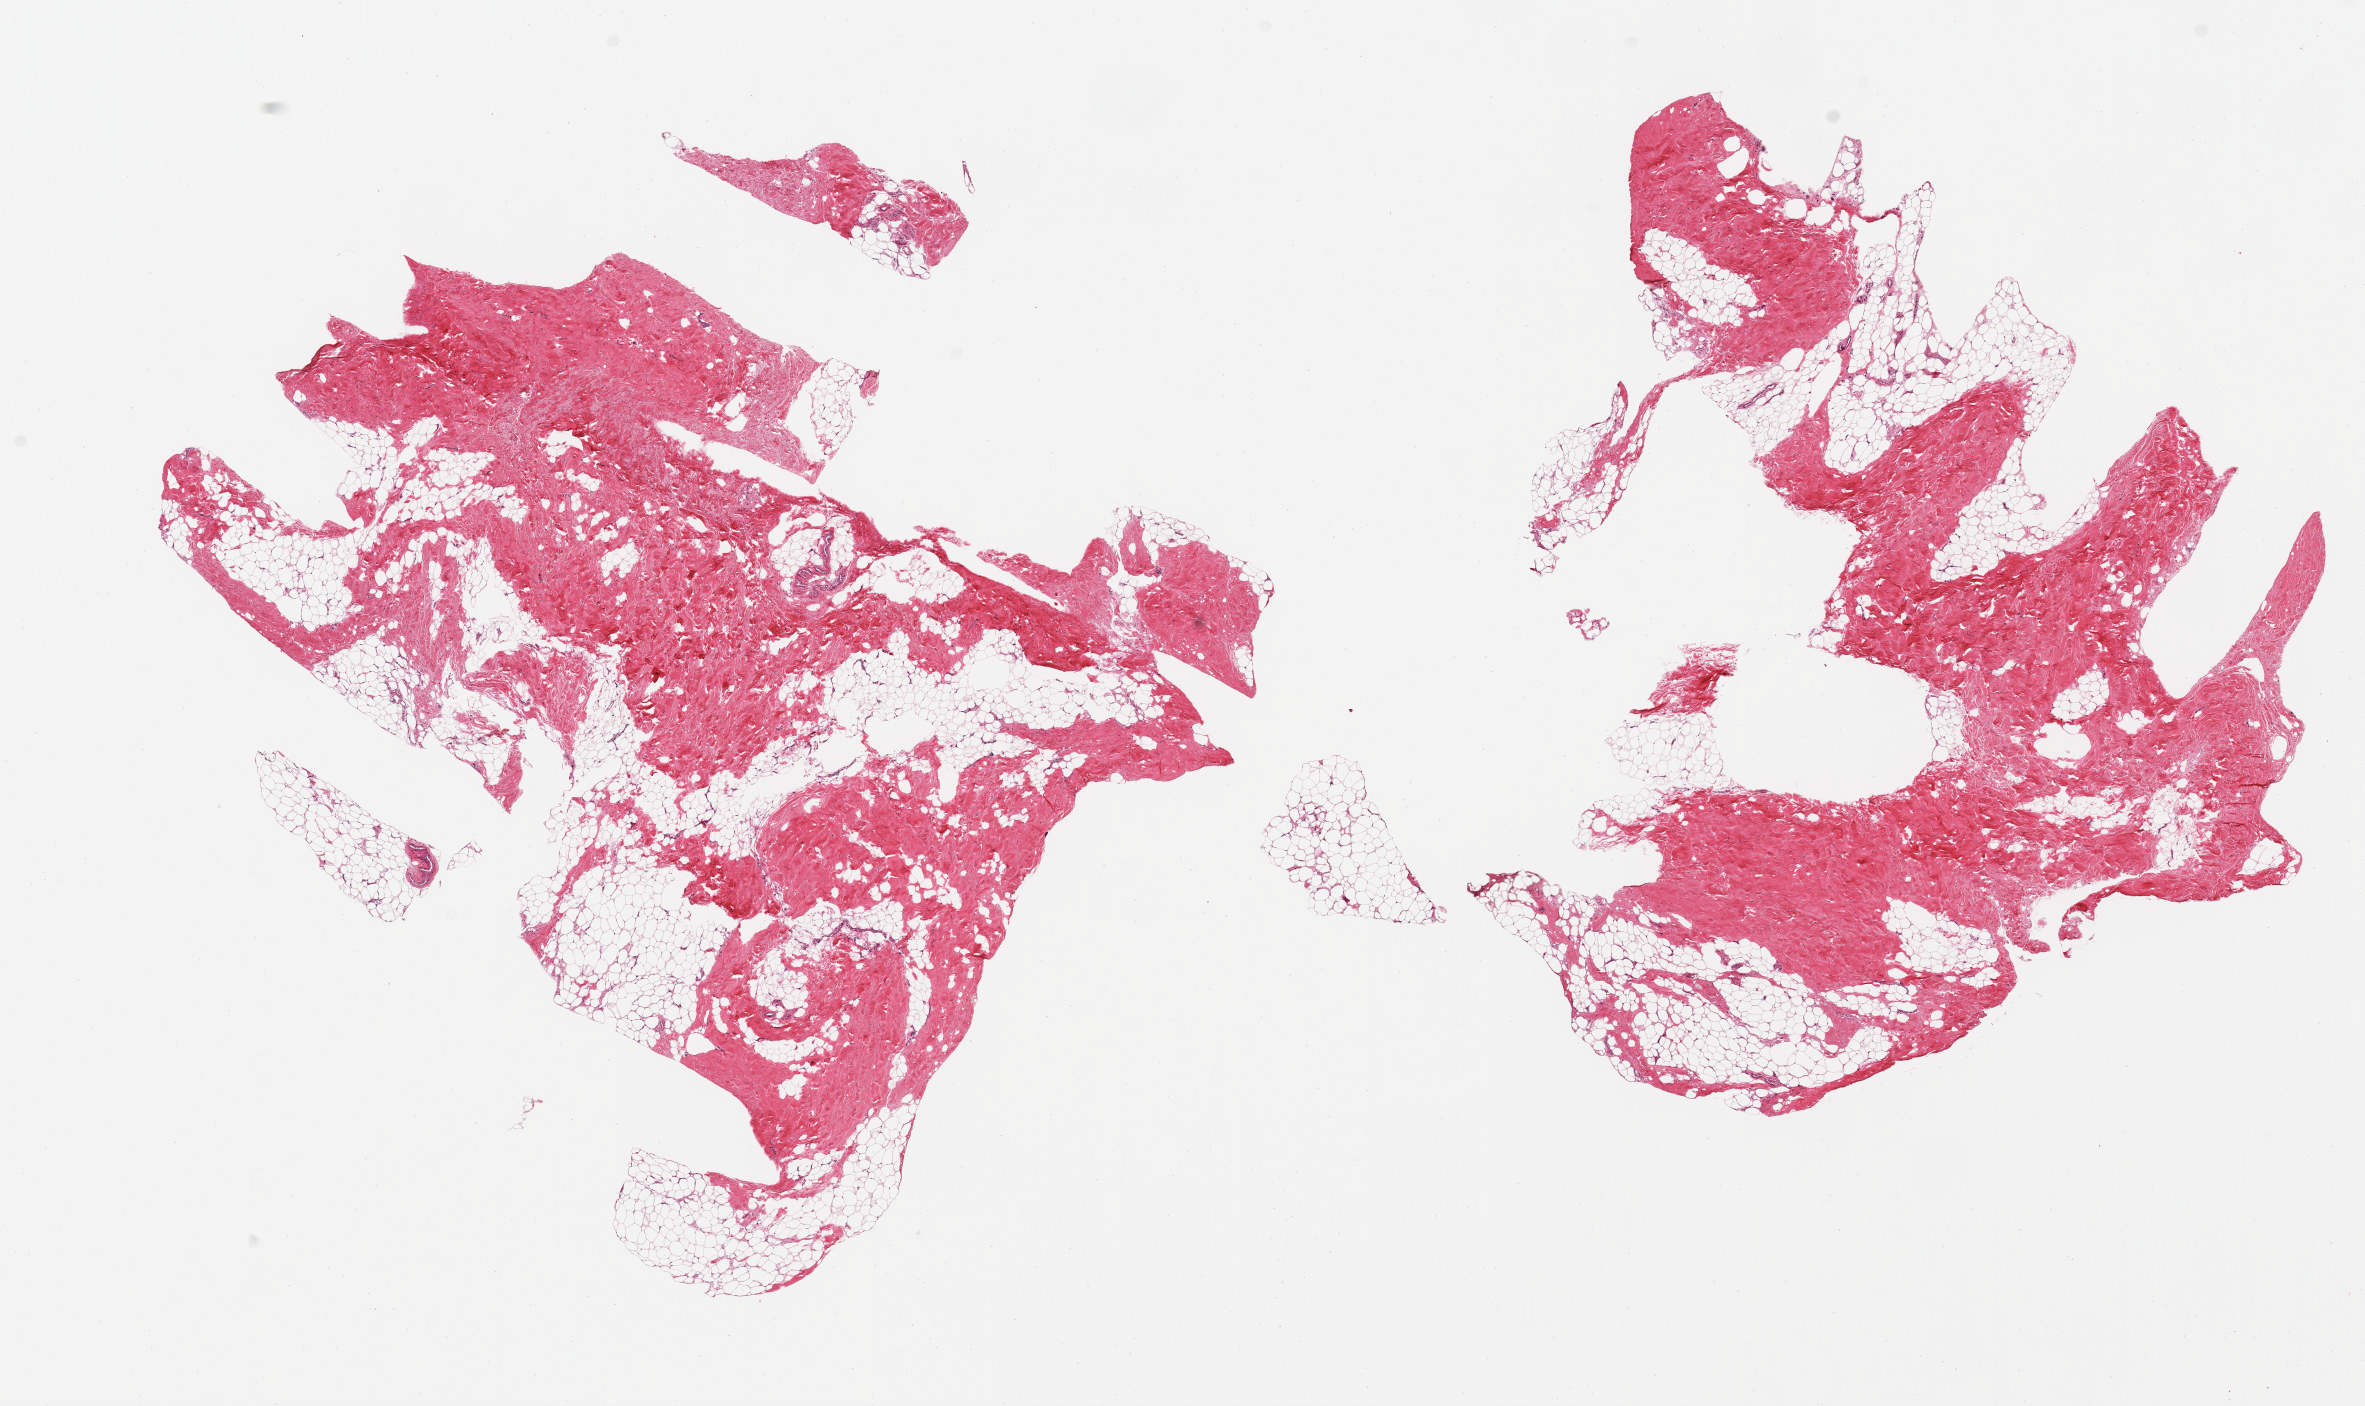
Digitized hematoxylin and eosin (H&E)-stained section, shown as a low-resolution overview of the whole scanned area (about 18.7 x 11.1 mm). PAXgene-fixed, paraffin-embedded tissue. Sampled site (target tissue): breast. Donor tissue sample. Donor sex: male.
* reviewer comment on this tissue sample: 2 pieces, fibroadipose elements only